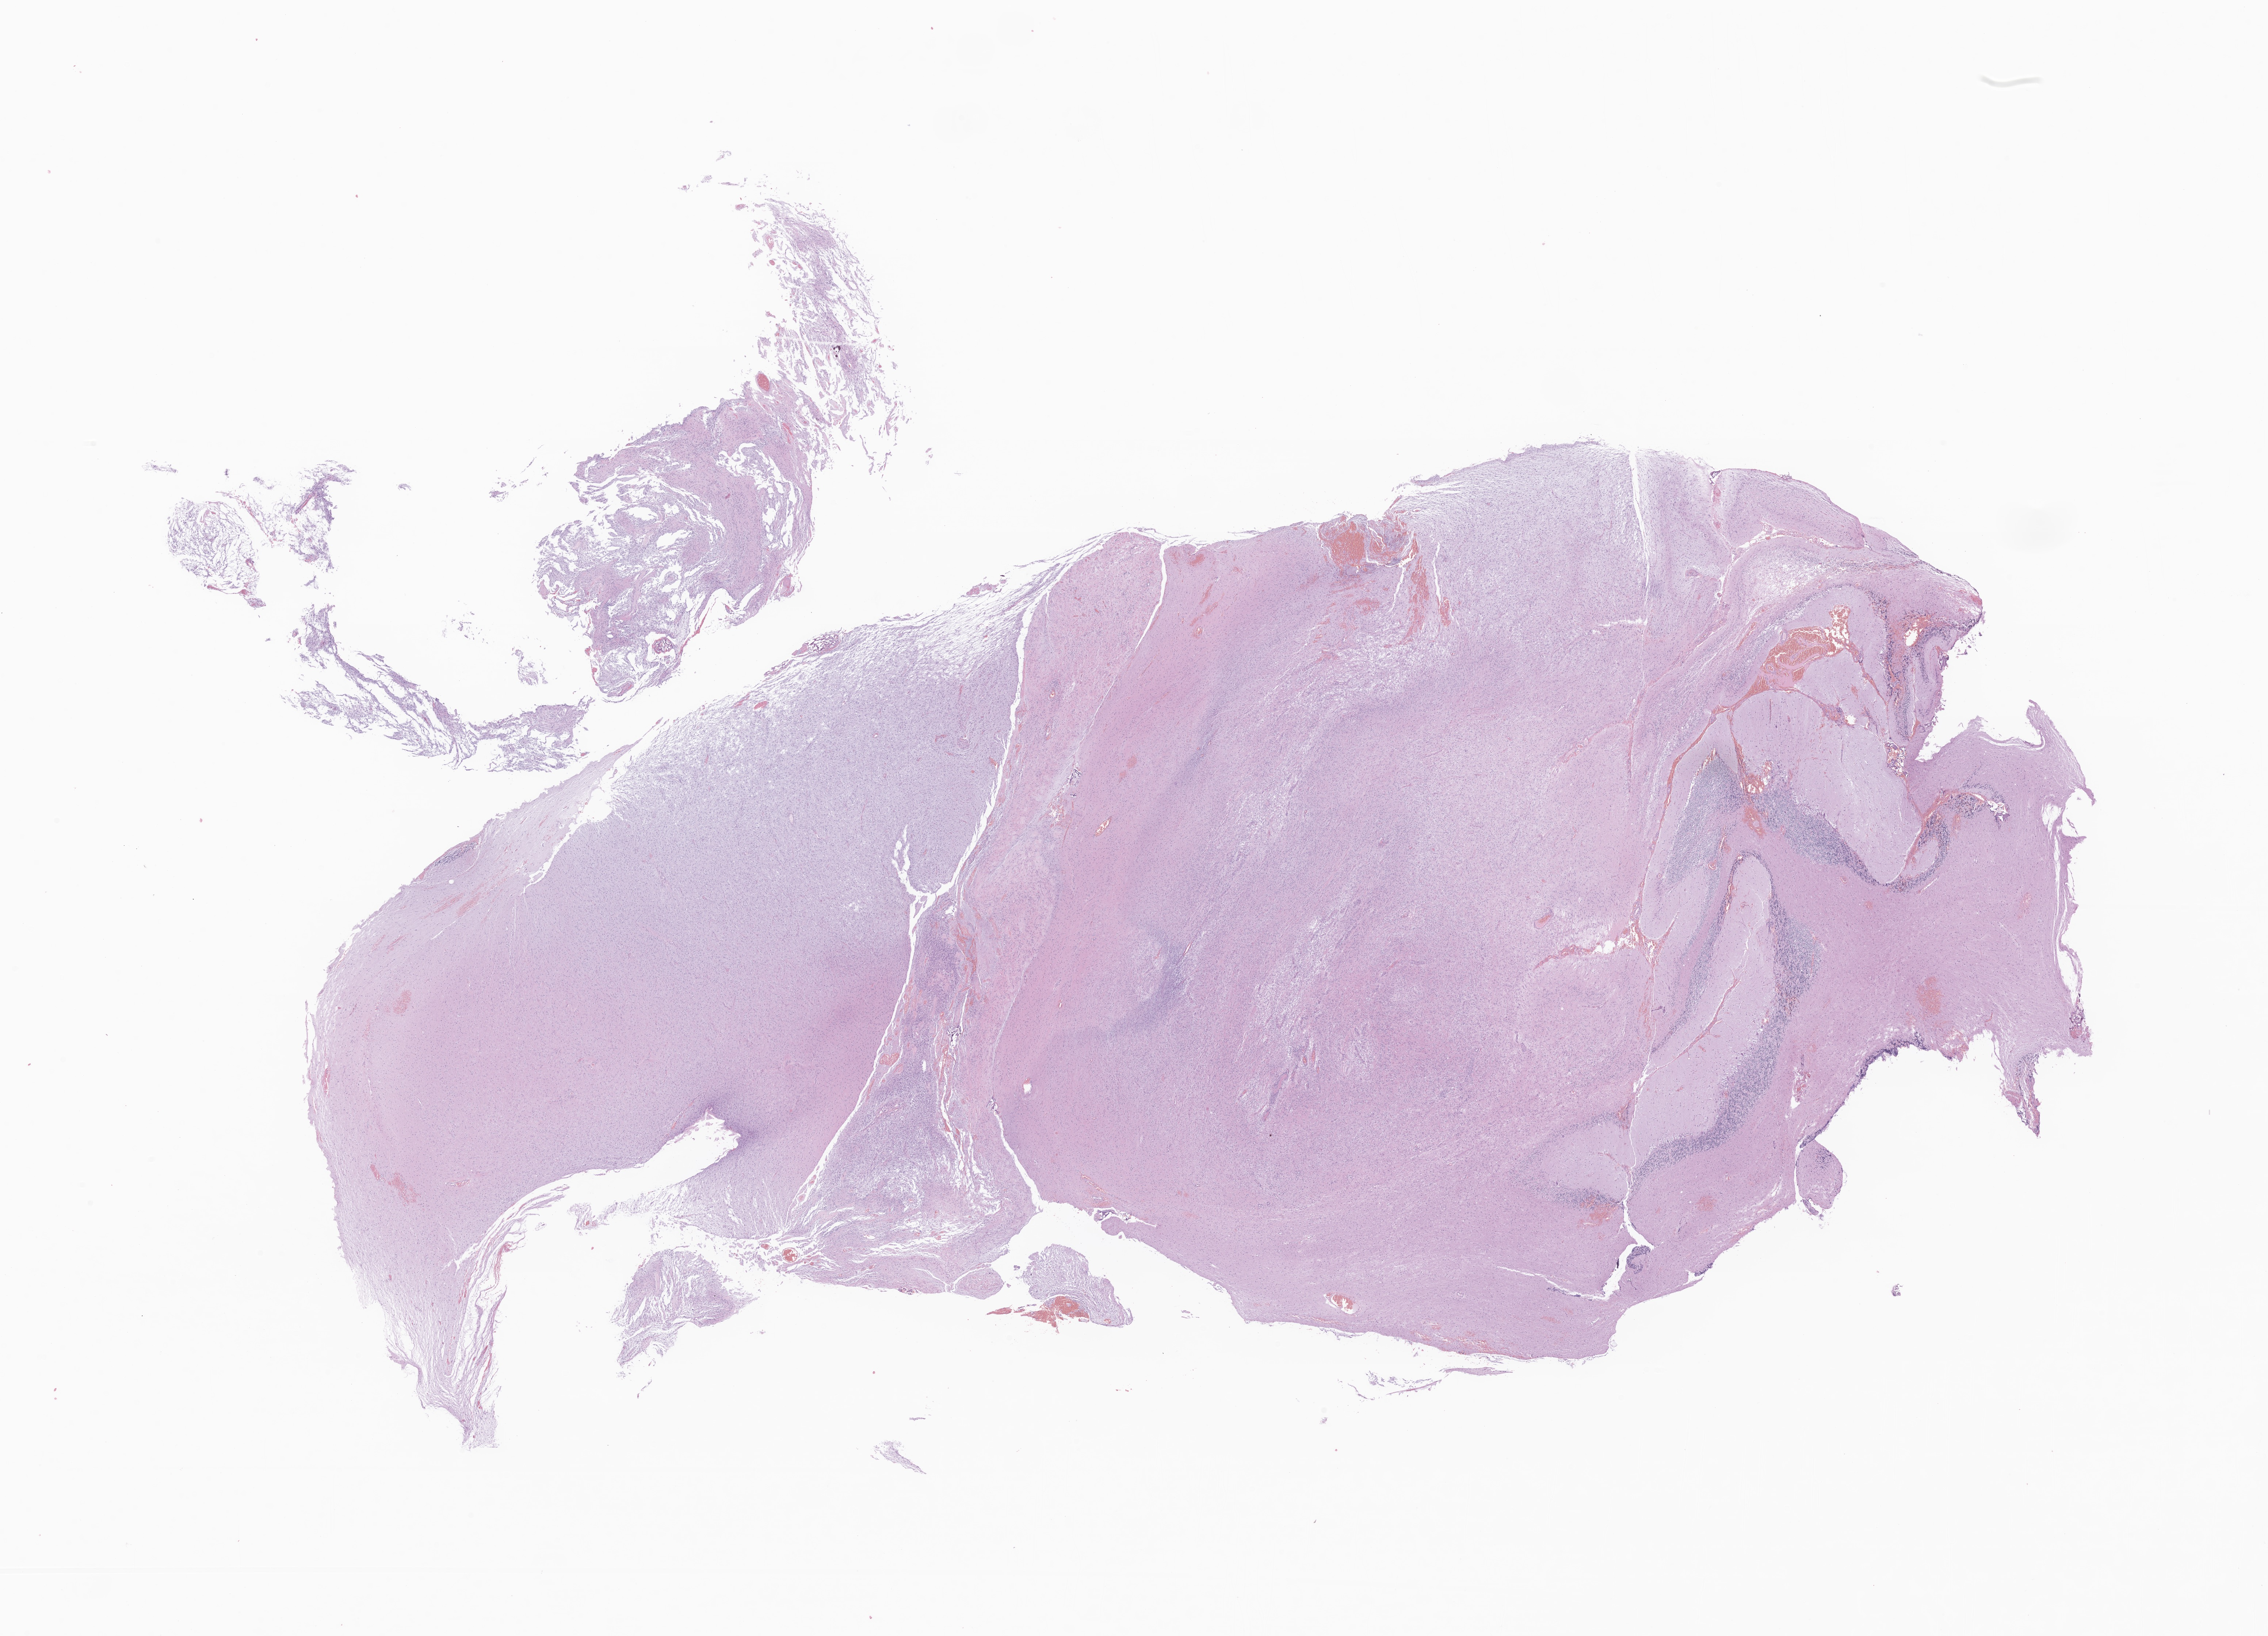
Haematoxylin and eosin whole-slide image of tumor tissue from the brain — a low-resolution overview of the entire scanned area, about 26.2 x 18.9 mm, formalin-fixed paraffin-embedded section. Patient female; age 132 months (11 years).
Diagnosis (ICD-O-3 morphology term): Pilocytic astrocytoma.